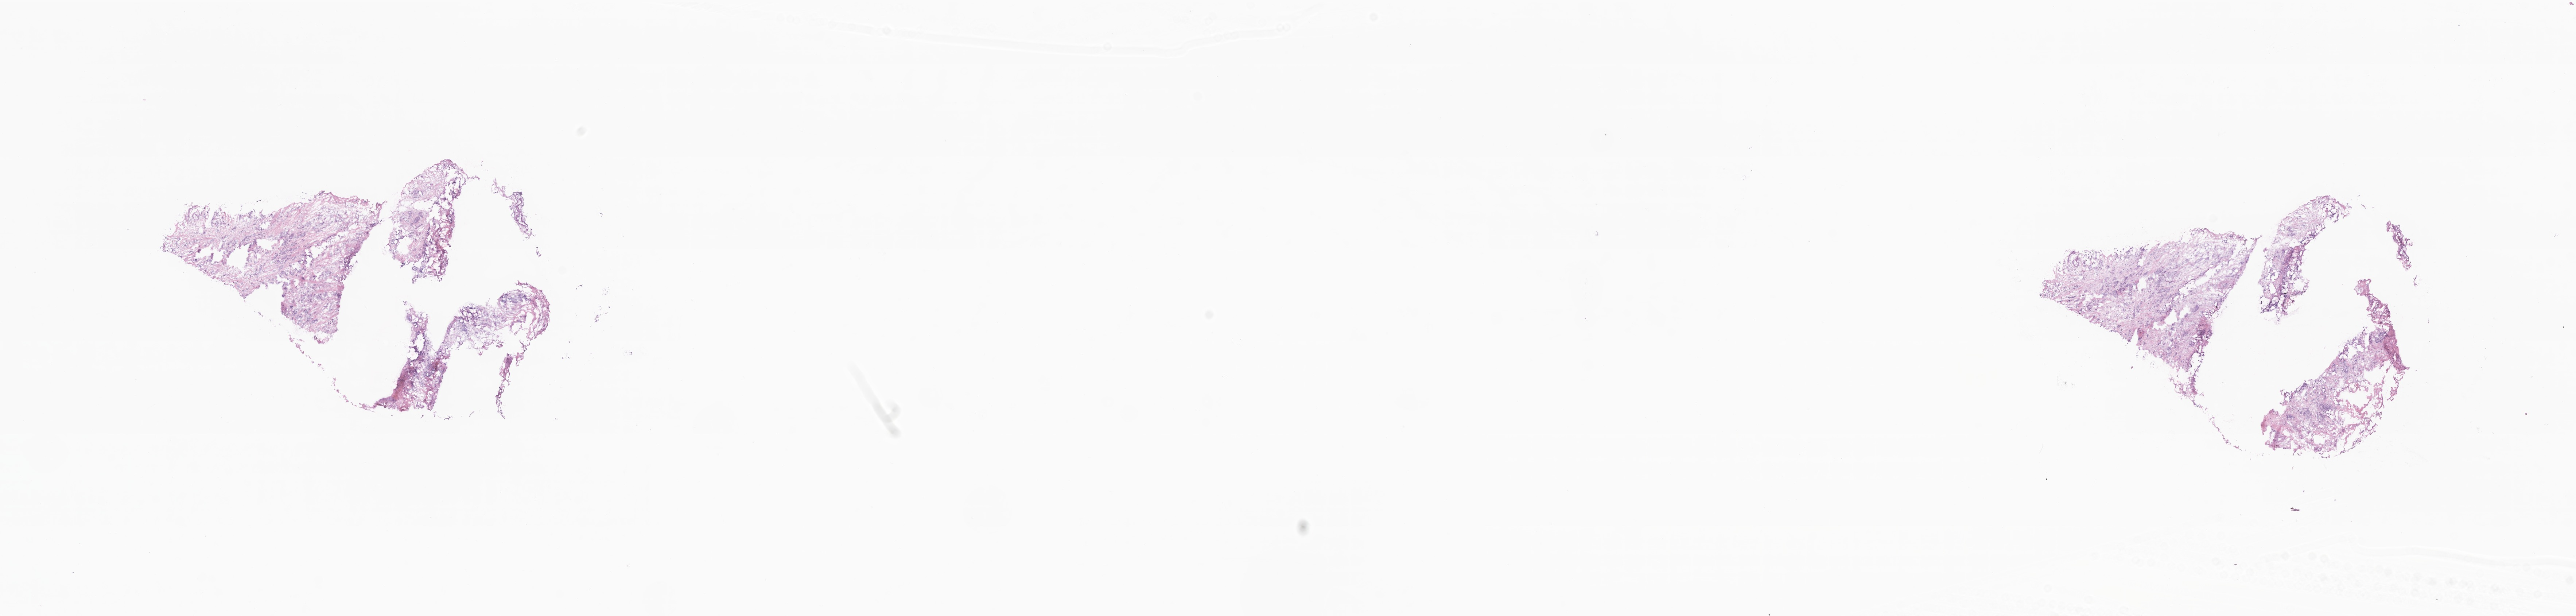
Digitized haematoxylin and eosin-stained section — shown as a low-resolution overview of the whole scanned area (about 29.8 x 7.1 mm). Frozen section. Primary tumor. Anatomic site: breast. Female, age 82 years at initial diagnosis. Slide review estimates, as recorded: tumor cells 15%, tumor nuclei 30%, stromal cells 15%, necrosis 0%, normal cells 70%. Infiltration values recorded for this section: lymphocyte infiltration 0%, monocyte infiltration 0%, neutrophil infiltration 0%.
Histologic diagnosis: Infiltrating duct carcinoma, NOS. Section: top of the tissue portion.